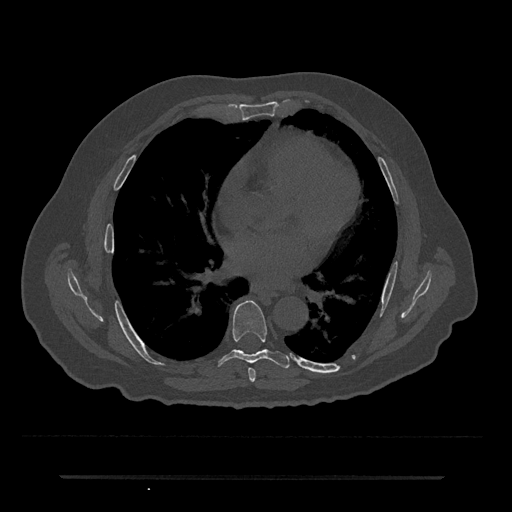
CT including the spine, one axial slice. Reconstruction kernel Br40s/3. 120 kVp. Bone window (W 1800 / L 400 HU). 0.5 mm slice thickness. 512 × 512 image matrix, field of view 437 × 437 mm. Male patient, age 69 years. Case-level facts recorded for this patient, not image findings: primary cancer: prostate.
Annotated regions visible in this slice (semi-automatically segmented with operator editing):
- T6 vertebra: bounding box [x1, y1, x2, y2] px = [248, 368, 256, 382]
- T7 vertebra: [218, 300, 290, 369]